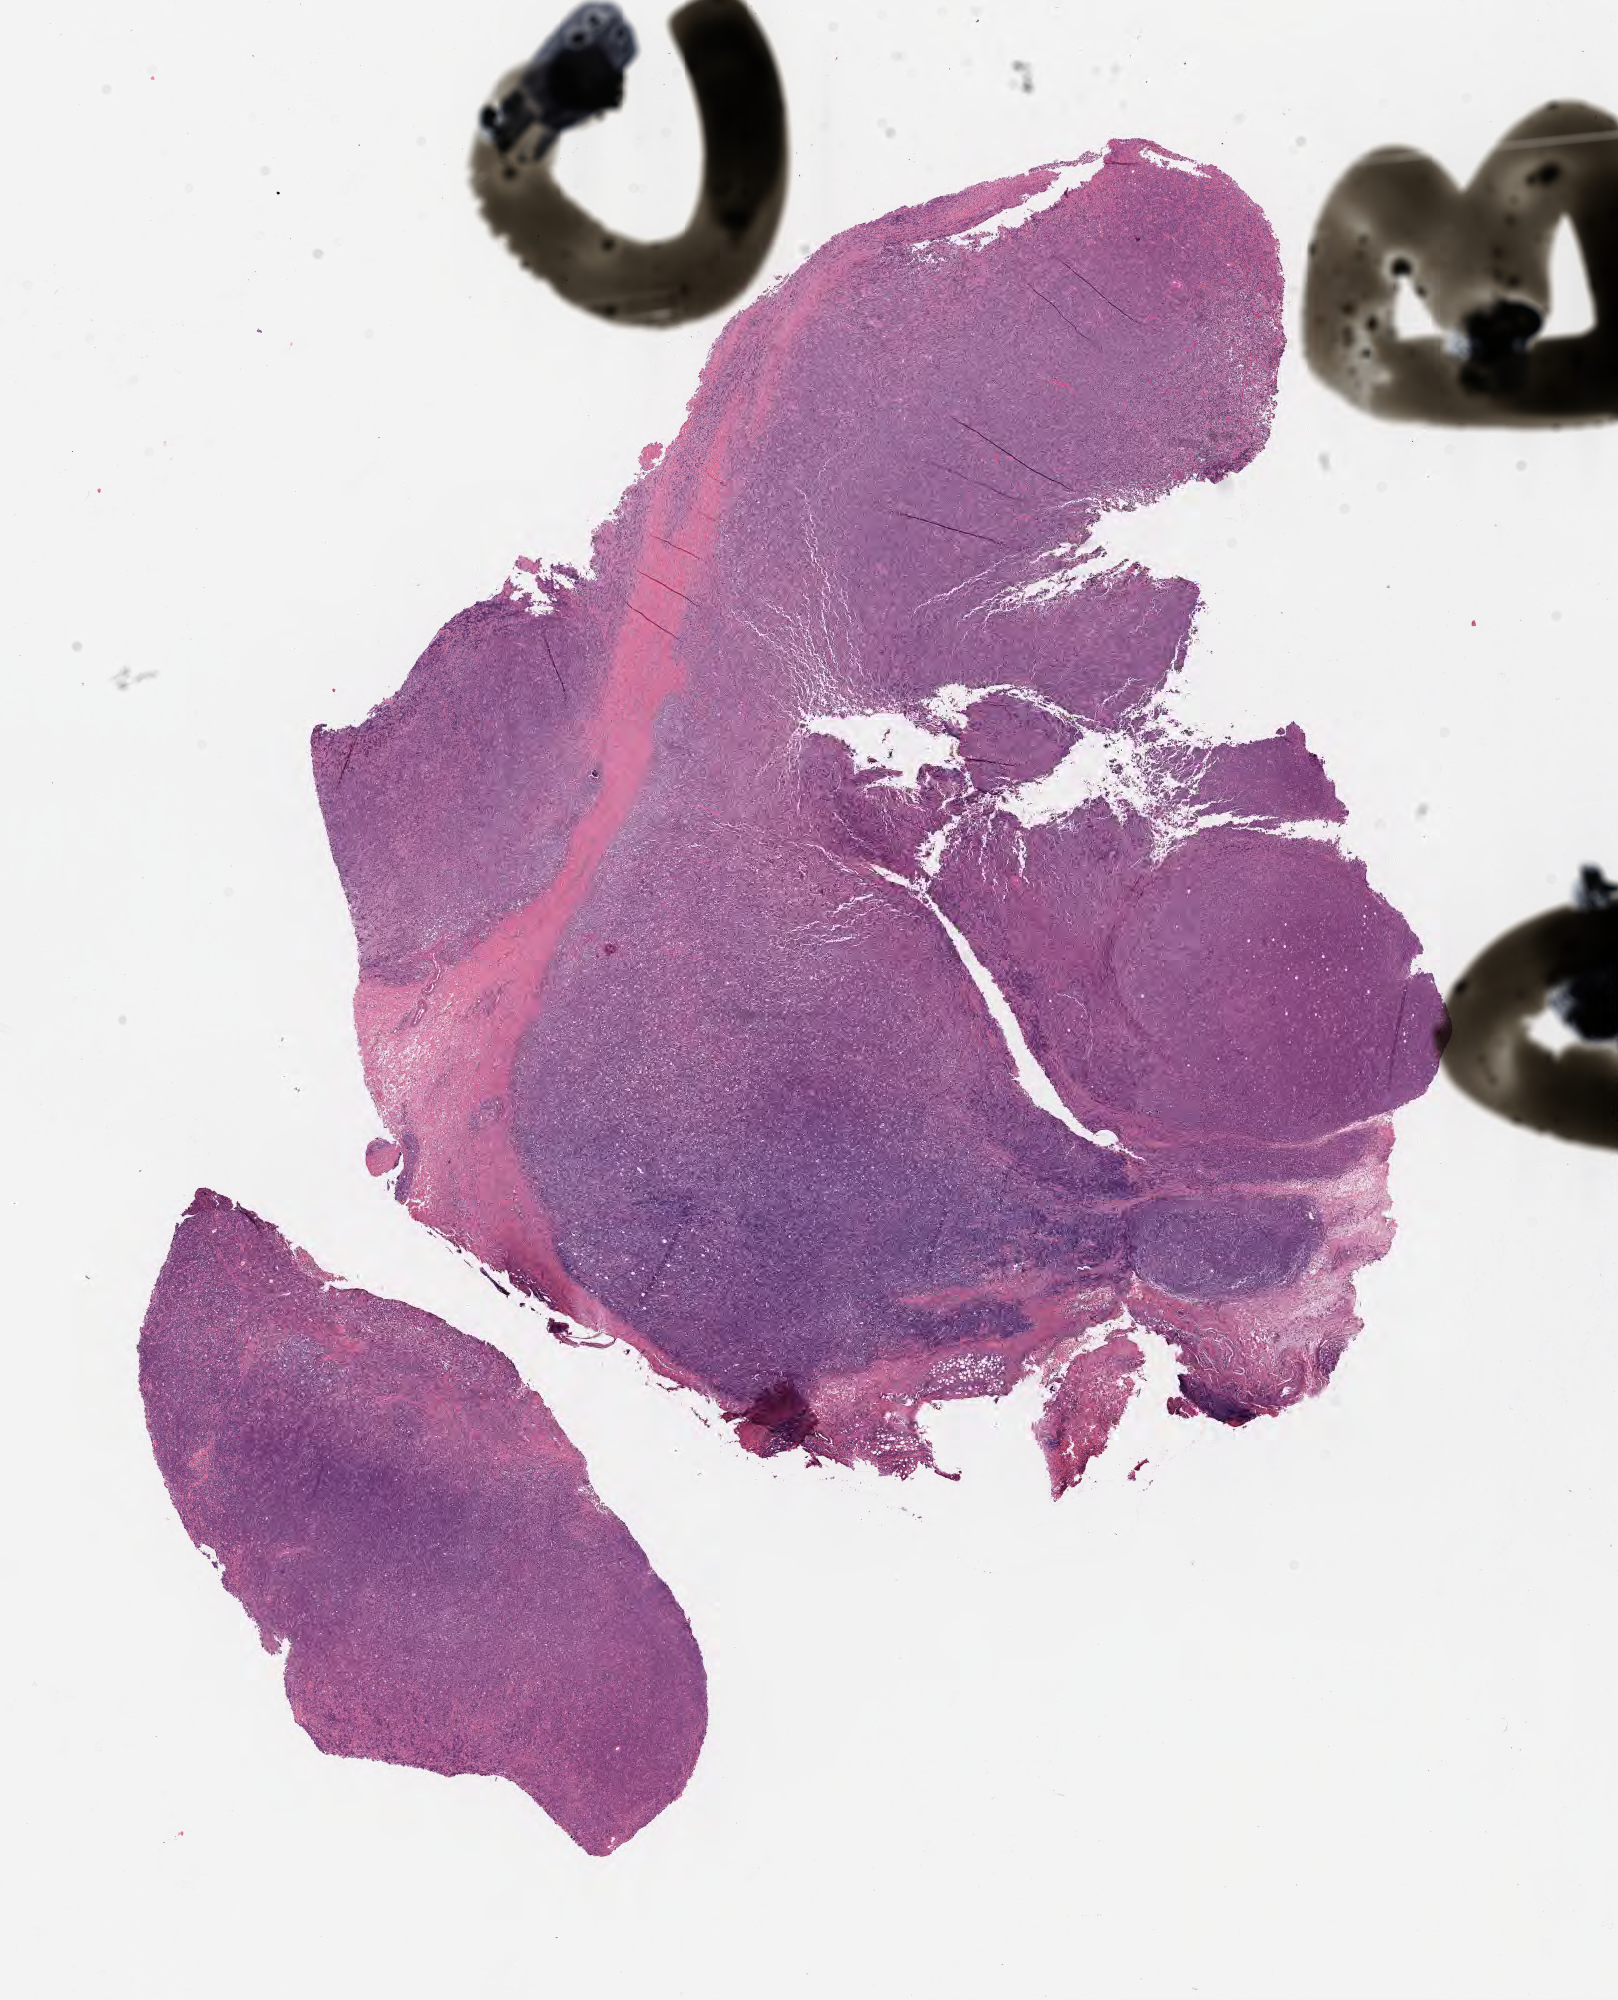
Digitized hematoxylin and eosin (H&E)-stained section — shown as a low-resolution overview of the whole scanned area (about 13.1 x 16.2 mm). Specimen: tumor tissue. Site: cranium. Male patient, age 12 years.
Diagnosis: Diffuse large B-cell lymphoma, NOS.